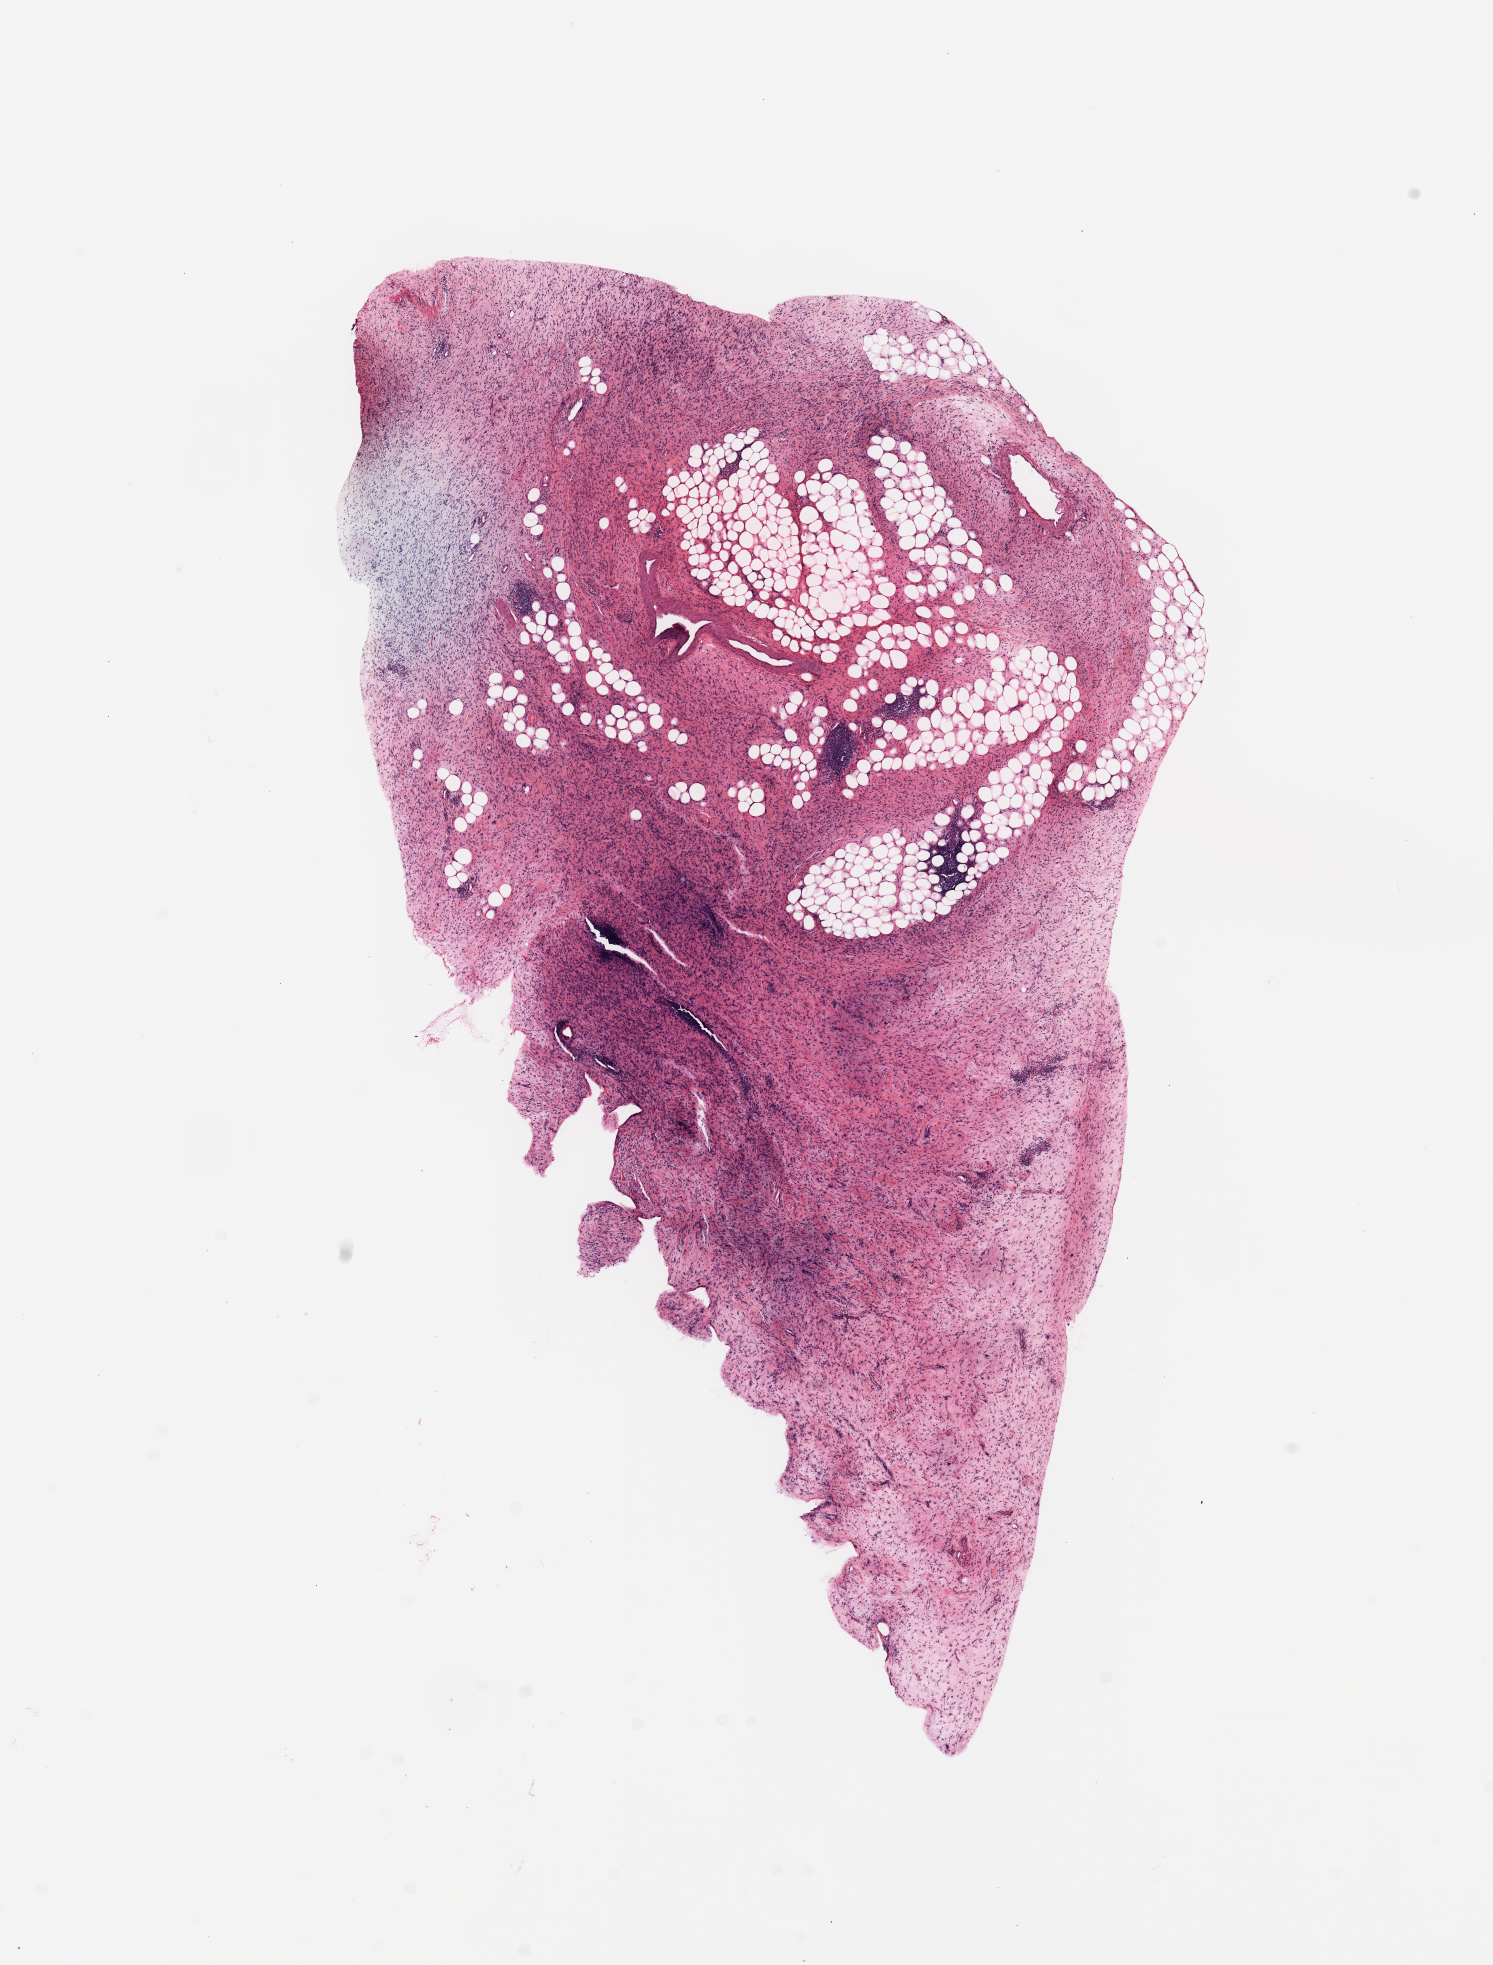
Digitized H&E-stained tissue section (whole slide) — shown as a low-resolution overview of the whole scanned area (about 11.8 x 15.5 mm, acquisition: 20x scan), tumour tissue sample. 52-year-old male patient.
Primary tumour site (as recorded): retroperitoneum. Patient diagnosis (cohort enrolment): sarcoma (site not recorded at cohort level).